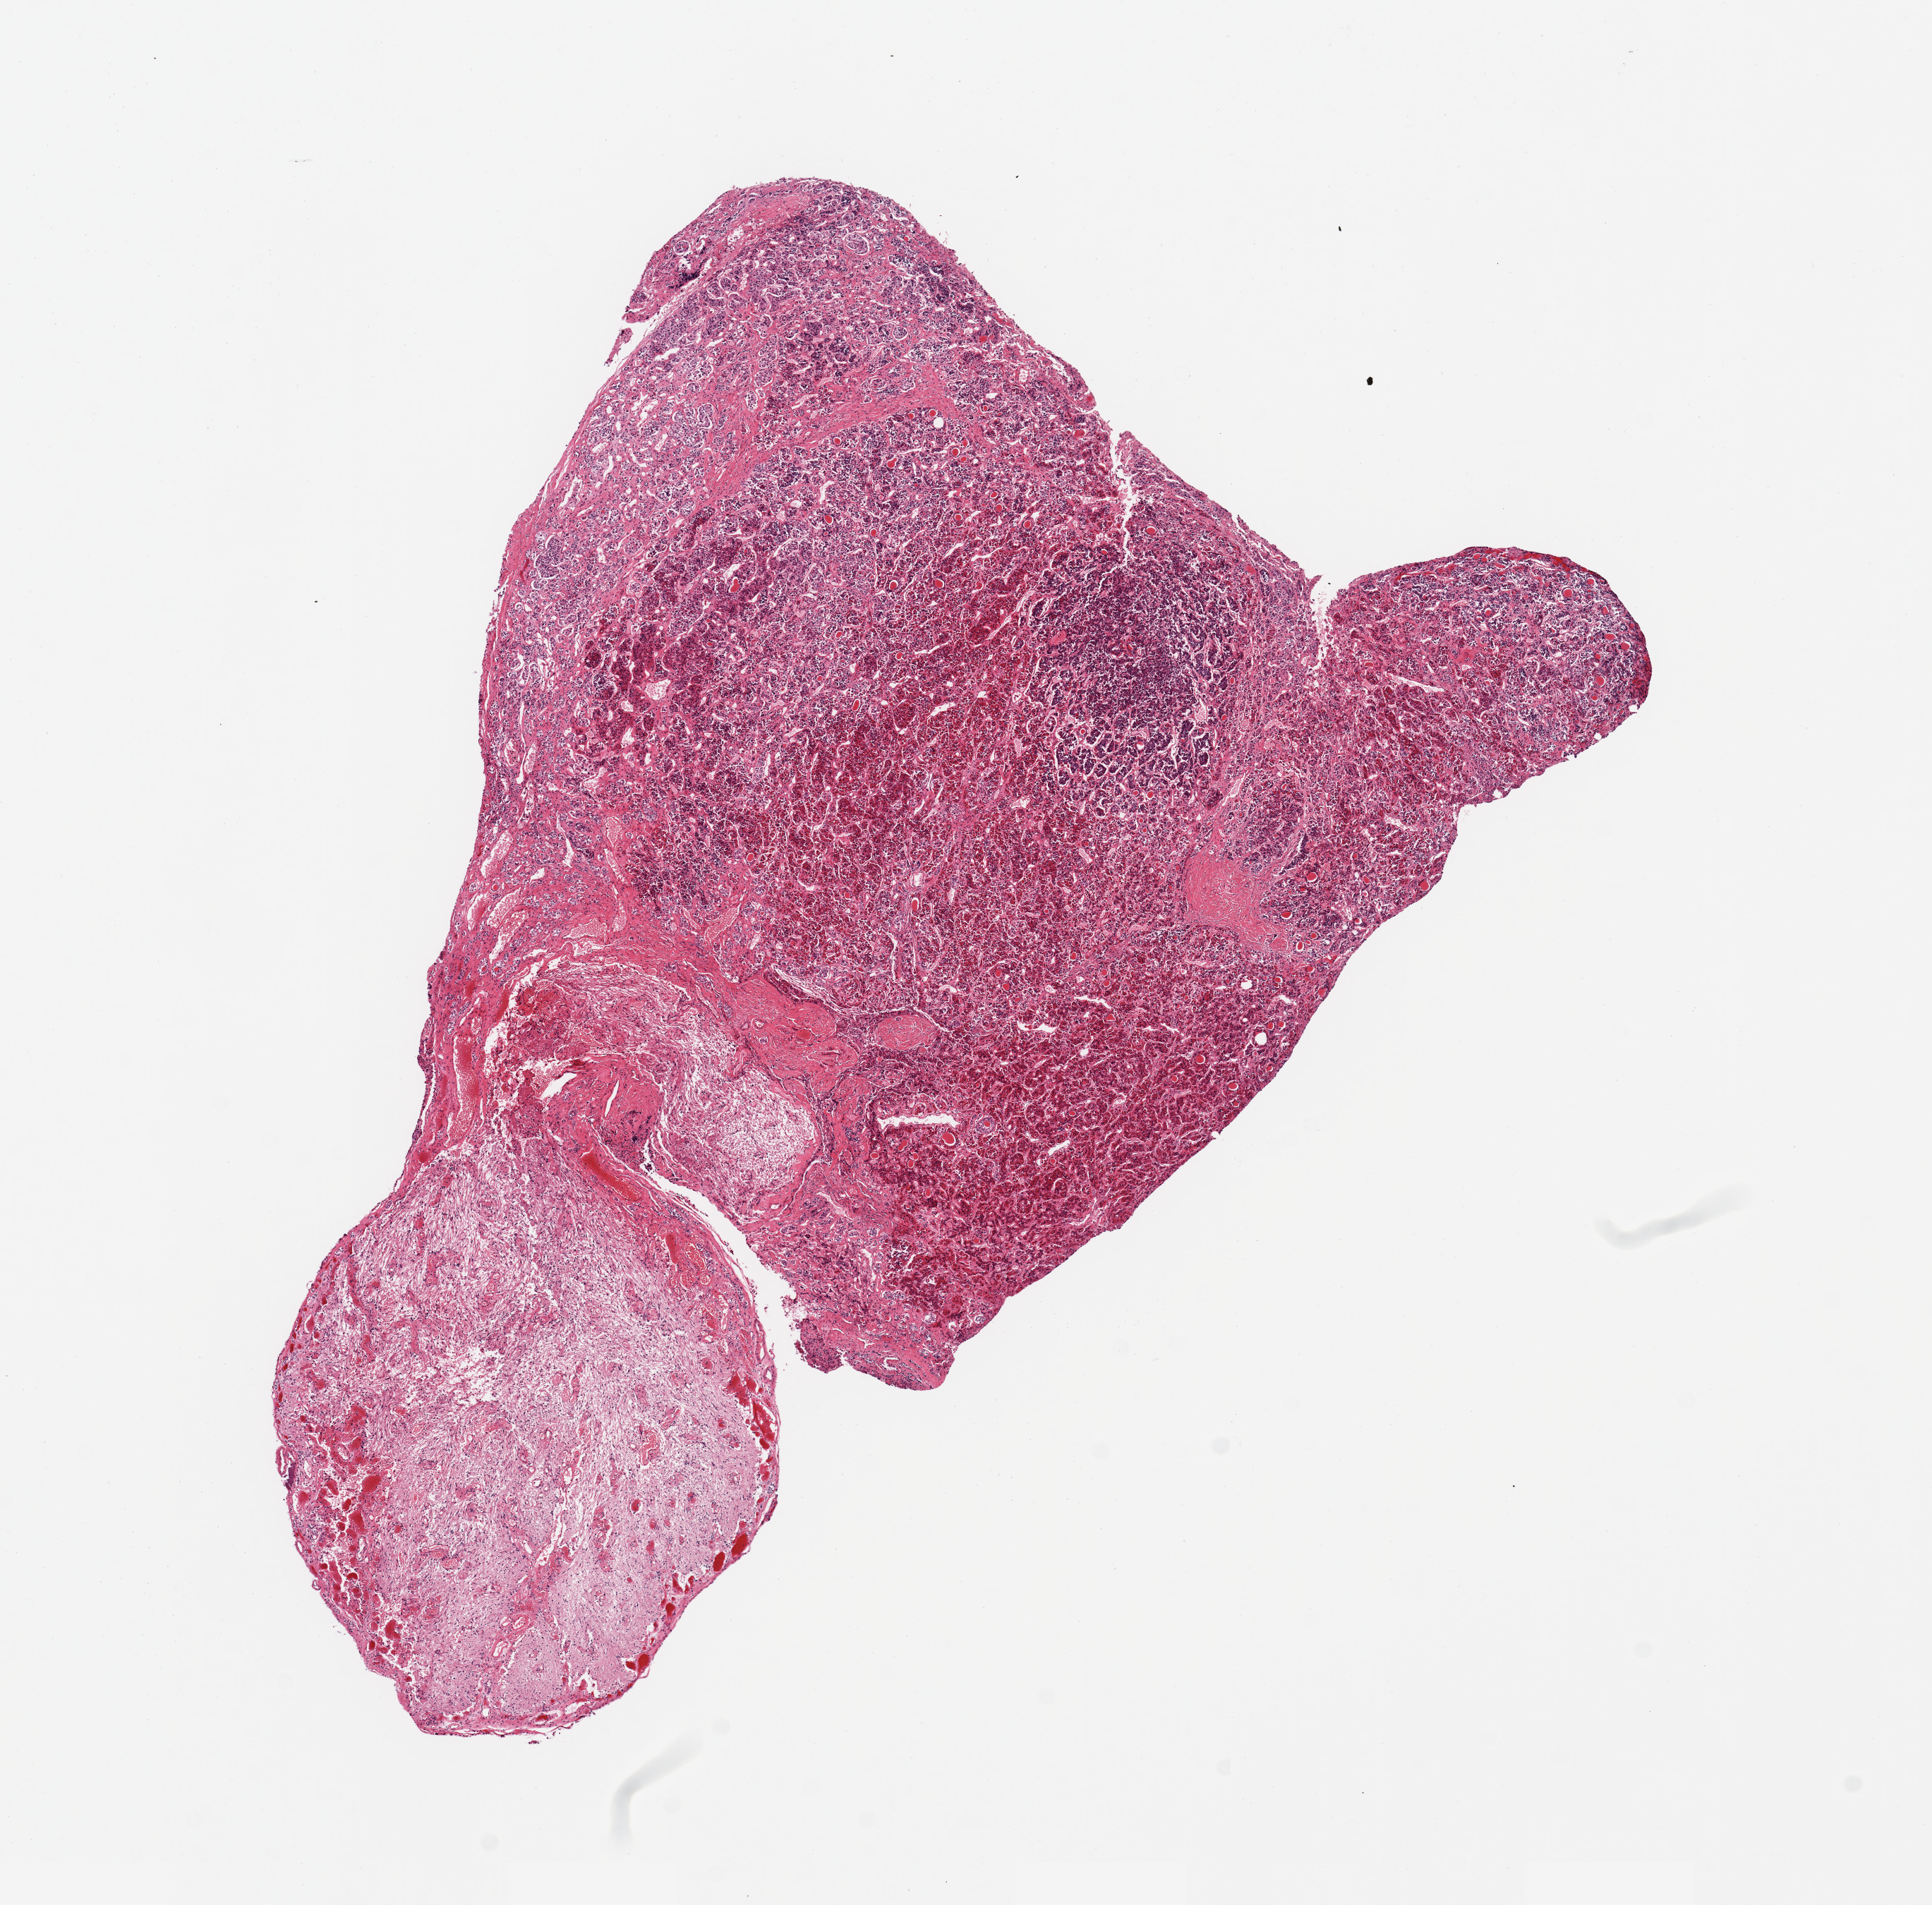
Whole-slide image, haematoxylin and eosin stain, brightfield, whole scanned area (about 10.8 x 10.7 mm) shown as a low-resolution overview, PAXgene-fixed, paraffin-embedded tissue, sampled site (target tissue): pituitary, donor tissue sample. Donor: female.
Review note (as recorded): 1 piece, ~25% neurohypophysis; rest is adenohypohypophysis.